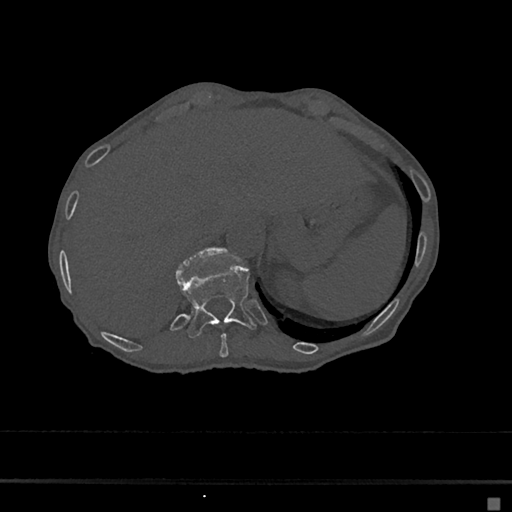
CT including the spine, one axial slice; position 180 of 797 along the scan axis; reconstruction kernel Br40s/3; bone window (W 1800 / L 400 HU); 0.5 mm slice thickness; 512 × 512 image matrix, field of view 360 × 360 mm. Patient: female, 68 years. From the clinical record (not read from this slice): primary cancer: renal.
Structures marked on this image (semi-automatic segmentation, software-assisted and operator-edited):
- T10 vertebra: bounding box <220,333,228,358> (left, top, right, bottom; pixels)
- T11 vertebra: <176,264,256,339>
- T12 vertebra: <179,248,222,268>